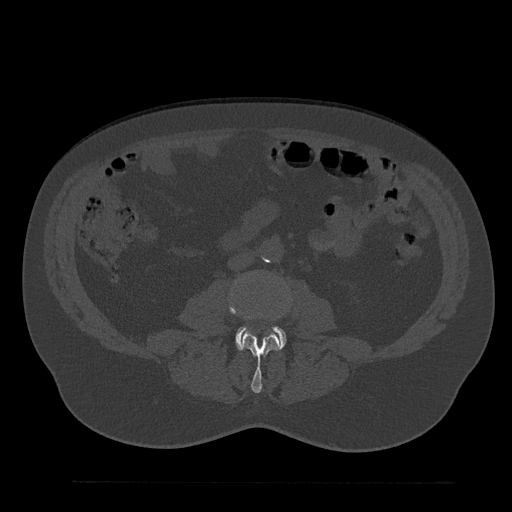
CT including the spine, one axial slice; slice 5 of 797 in the series (ordered by position); reconstruction kernel Br40s/3; 120 kVp; bone window (W 1800 / L 400 HU); 0.5 mm slice thickness; 512 × 512 image matrix. Male patient, age 61 years. From the clinical record (not read from this slice): primary cancer: prostate.
Annotated regions visible in this slice (semi-automatic segmentation, software-assisted and operator-edited):
- L3 vertebra: box from (x=229, y=301) to (x=289, y=393) px
- L4 vertebra: (x=236, y=326)–(x=286, y=349)